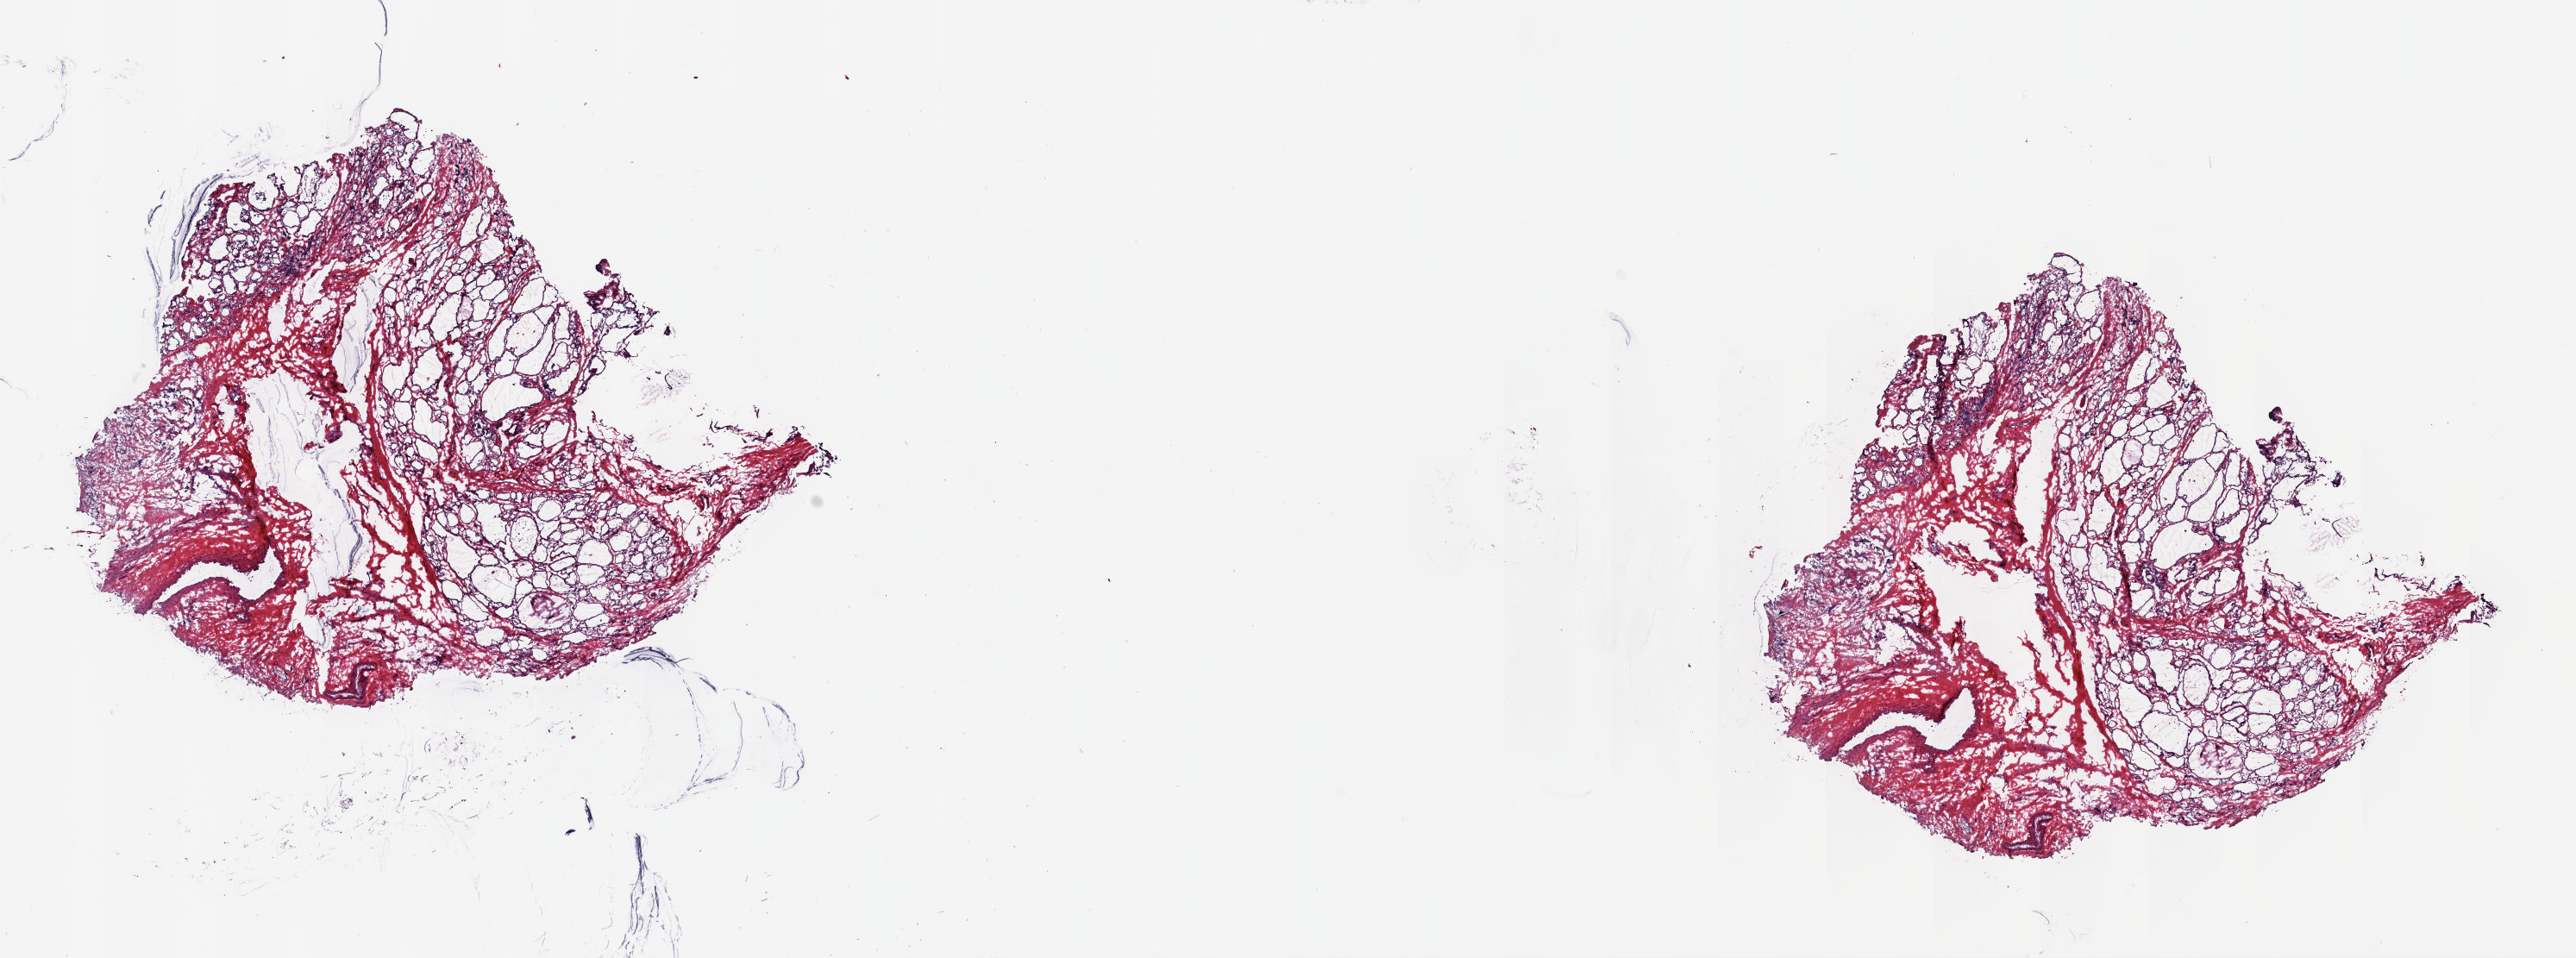
H&E-stained whole-slide image, low-resolution overview of the scanned area, about 23.6 x 8.8 mm. Frozen section from the top of the tissue portion. Thyroid, solid tissue normal (non-tumour tissue) sample. Patient: female, age at initial diagnosis 34 years. Pathologist review of this section (percent, as recorded): tumour cells 0%, tumour nuclei 0%, normal cells 100%, stromal cells 0%, necrosis 0%. Inflammatory infiltration, as recorded: lymphocyte infiltration 2%, monocyte infiltration 0%, neutrophil infiltration 0%.
This section: solid tissue normal (non-tumour) sample from the same patient. Patient diagnosis: Papillary adenocarcinoma, NOS.